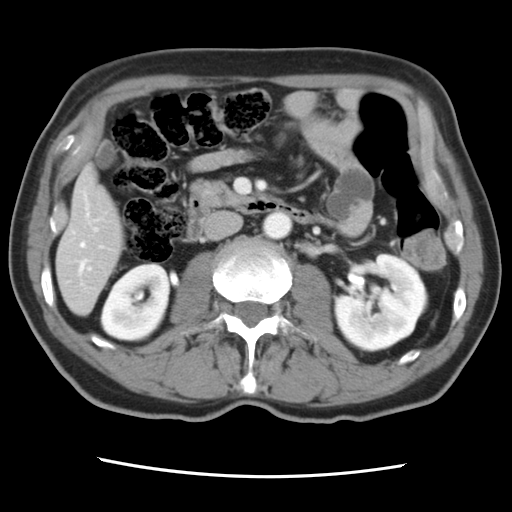
Contrast-enhanced abdominal CT, one axial slice; position 28 of 83 along the scan axis; intravenous contrast given; soft-tissue window (W 400 / L 40 HU); 5 mm slice thickness; 512 × 512 image matrix. Male patient, age 69 years. From the clinical record (not read from this slice): diagnosis: colorectal cancer liver metastases, imaged before liver resection; multiple liver metastases: yes; largest metastasis: 3.5 cm.
Annotated regions visible in this slice (outlined manually by an expert reader):
- hepatic veins: bounding box <80,193,102,271> (left, top, right, bottom; pixels)
- liver: <58,170,123,314>
- planned liver remnant (the part of the liver to remain after resection): <58,170,123,314>
- portal vein (with intrahepatic branches): <89,229,98,270>